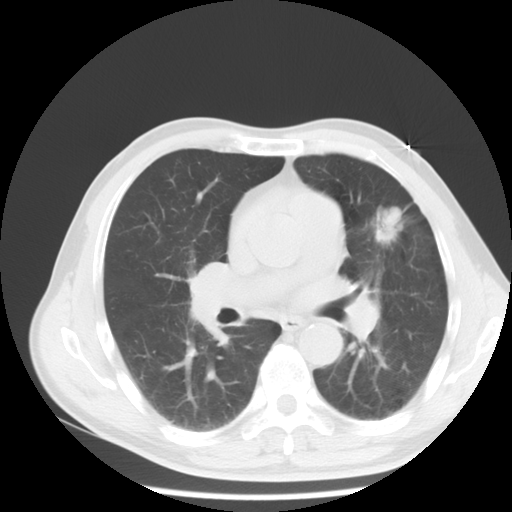
Chest CT, one axial slice. Slice 9 of 13 in the series (ordered by position). Reconstruction kernel STANDARD. Lung window (W 1500 / L -600 HU). 512 × 512 image matrix. Patient: male, 54 years. From the clinical record (not read from this slice): clinical TNM (as recorded): T1c N0 M0.
Outlined on this slice (bounding box drawn by a radiologist):
- lung tumour (recorded histology: adenocarcinoma): box from (x=369, y=203) to (x=406, y=246) px